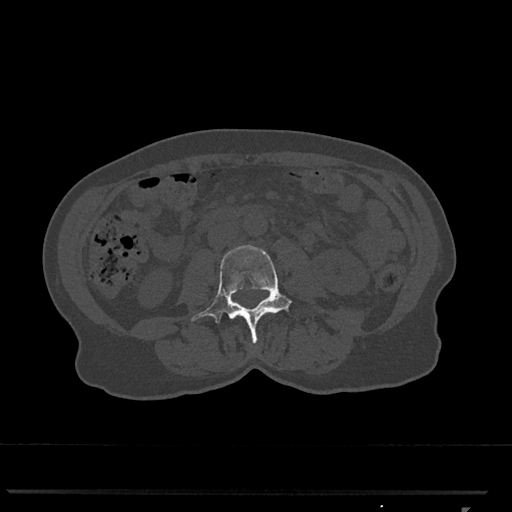
CT including the spine, one axial slice. Position 274 of 793 along the scan axis. Reconstruction kernel Br40s/3. 120 kVp. Bone window (W 1800 / L 400 HU). 512 × 512 image matrix, field of view 380 × 380 mm. Female patient, age 62 years. From the clinical record (not read from this slice): primary cancer: renal.
Outlined on this slice (semi-automatically segmented with operator editing):
- L3 vertebra: bounding box [x1, y1, x2, y2] px = [191, 245, 292, 343]